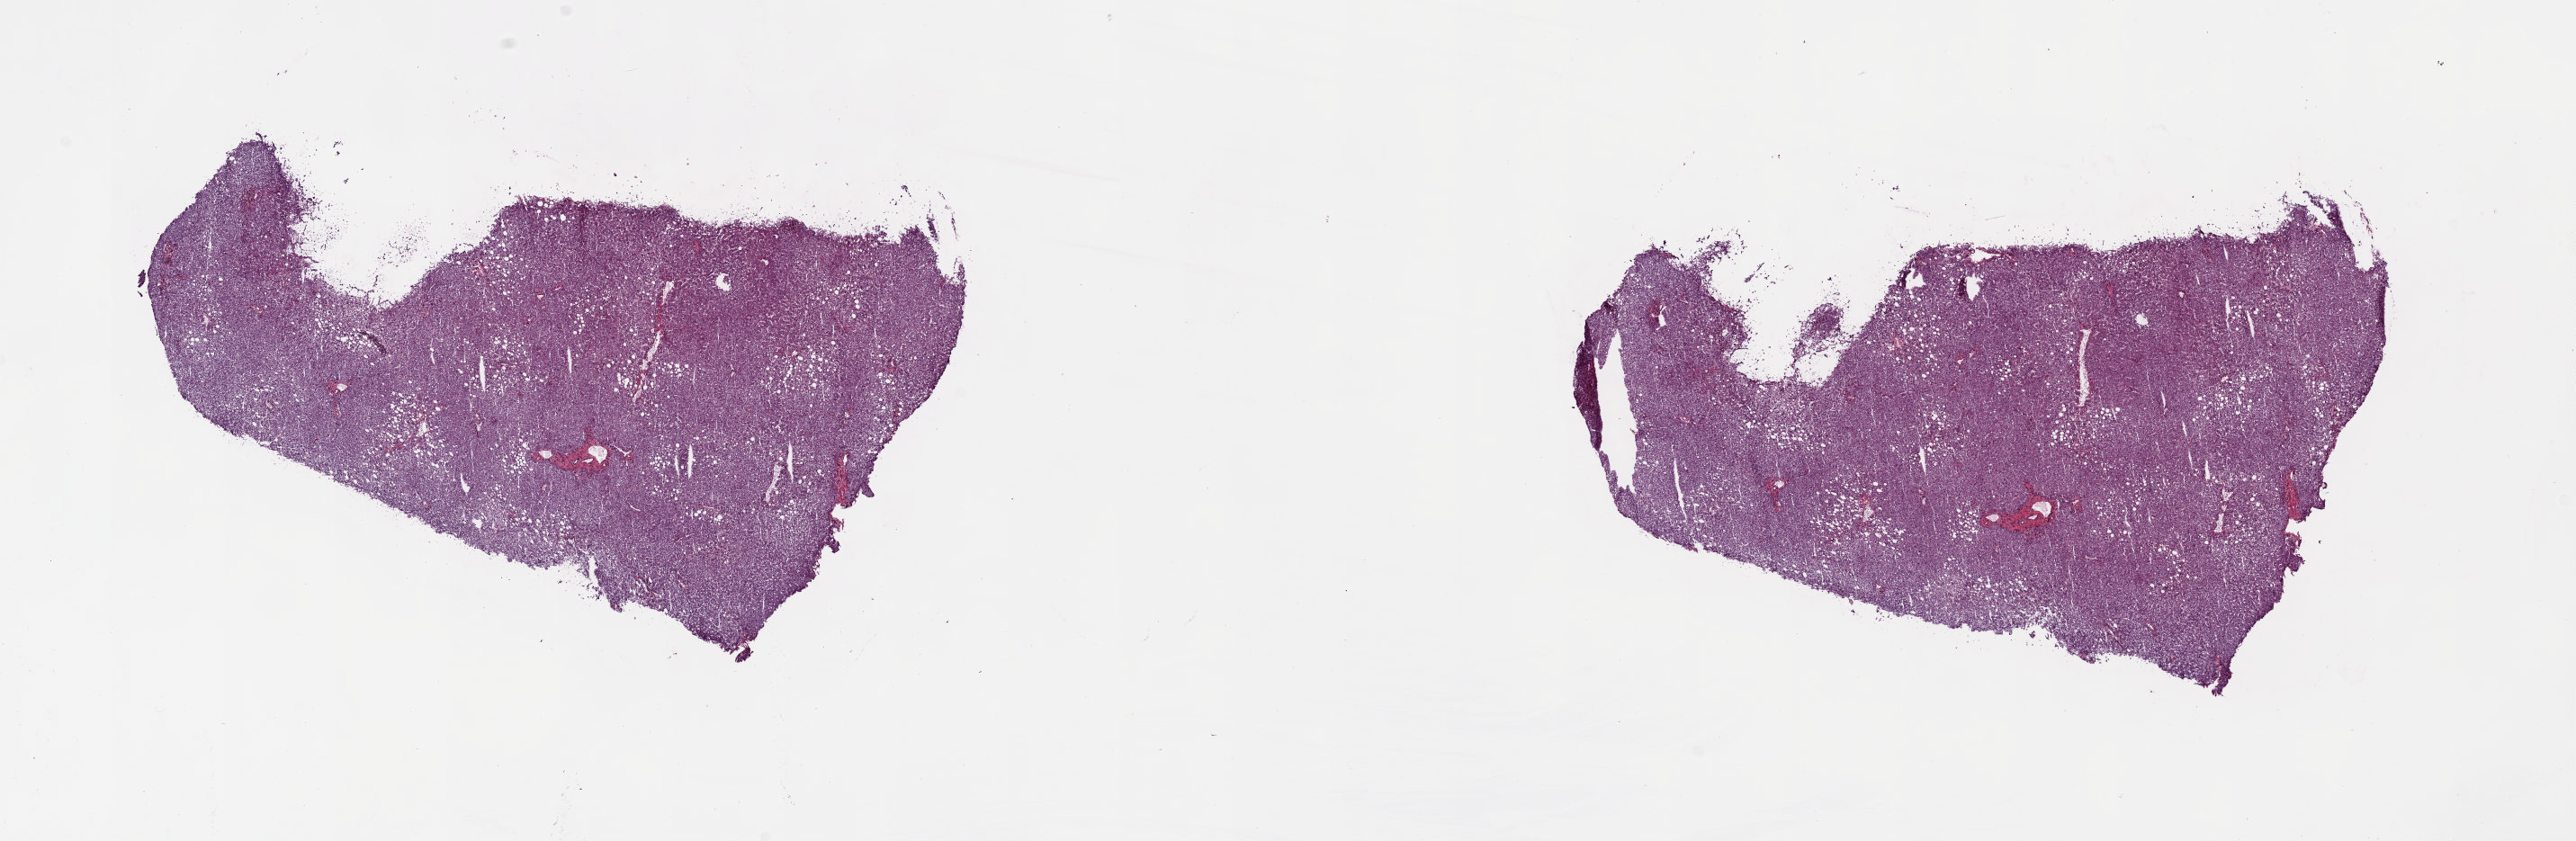
Whole-slide histology image, H&E — shown as a low-resolution overview of the whole scanned area (about 22.6 x 7.4 mm); frozen section from the top of the tissue portion; sample: solid tissue normal (non-tumour tissue), liver. Male, age 77 years at initial diagnosis. Slide review estimates, as recorded: tumour cells 0%, tumour nuclei 0%, normal cells 100%, stromal cells 0%, necrosis 0%. Inflammatory infiltration, as recorded: lymphocyte infiltration 2%, monocyte infiltration 1%, neutrophil infiltration 2%.
This section: solid tissue normal sample (biorepository sample class). Patient diagnosis: Hepatocellular carcinoma, NOS.